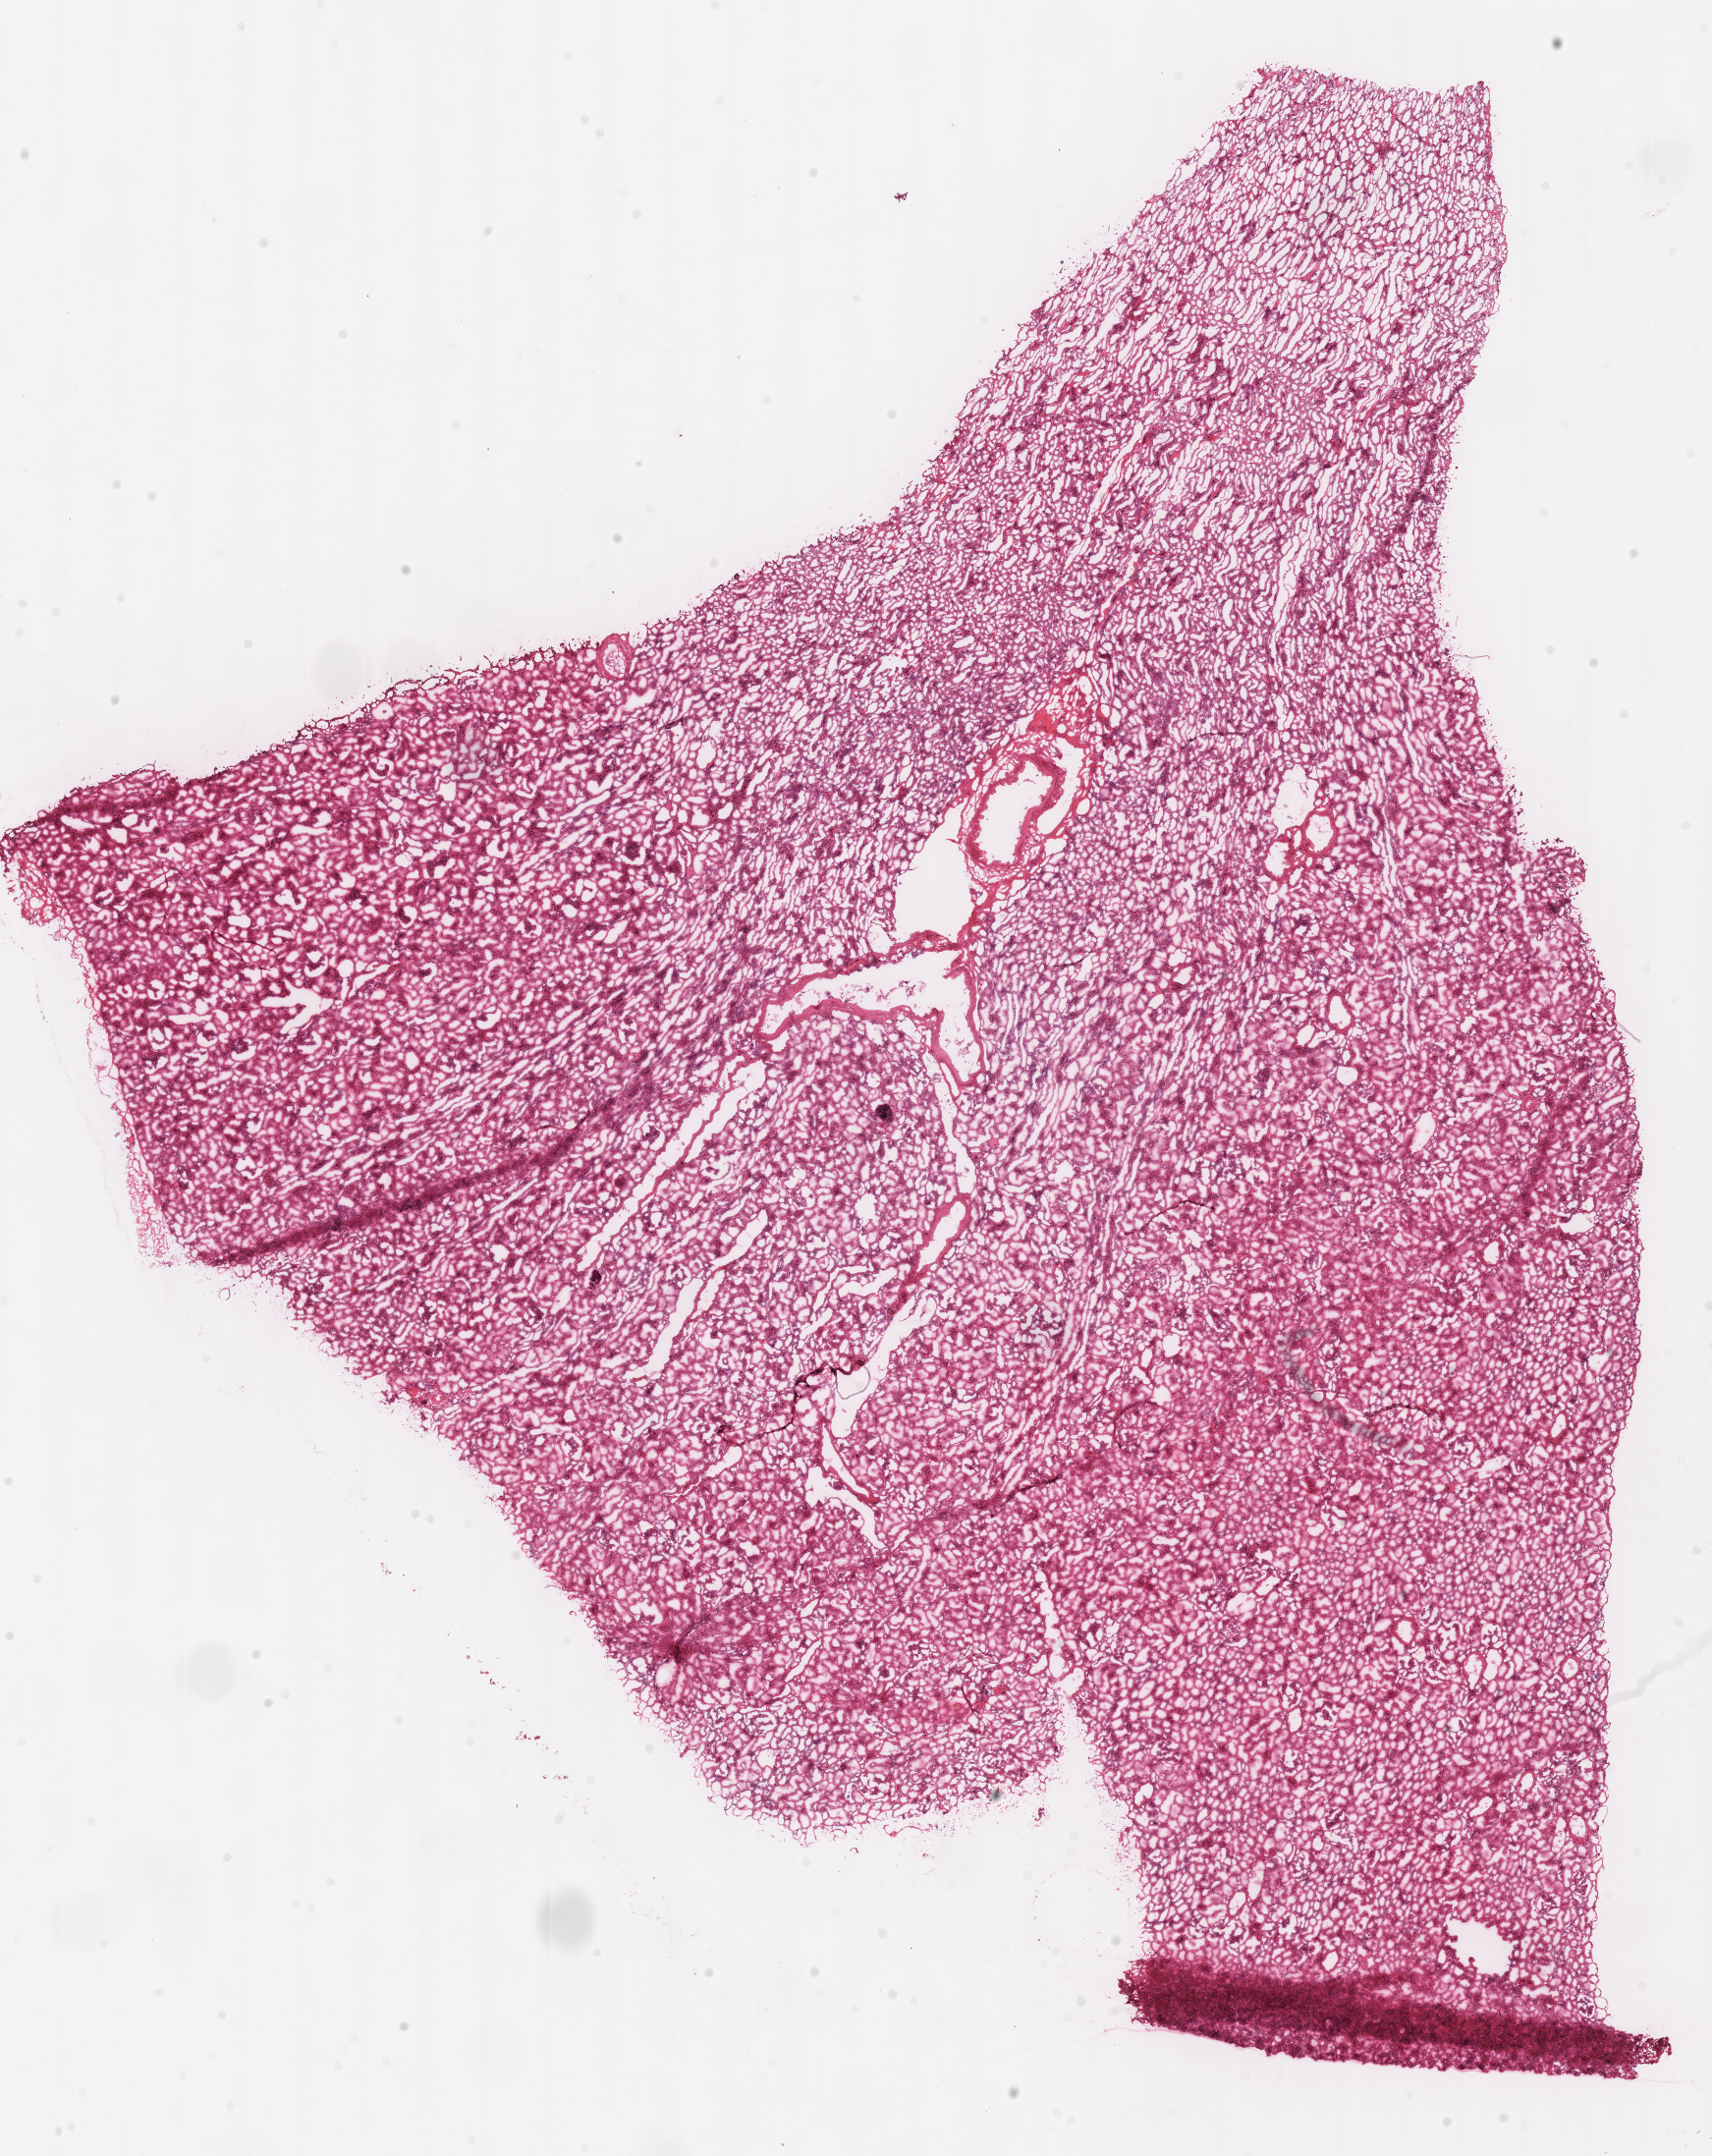
Whole-slide histology image, H&E, whole scanned area (about 13.7 x 17.3 mm) shown as a low-resolution overview; frozen section from the top of the tissue portion; sample: solid tissue normal (non-tumour tissue), kidney. Female patient; age at initial diagnosis 46 years. Inflammatory infiltration, as recorded: lymphocyte infiltration 1%, monocyte infiltration 0%, neutrophil infiltration 0%.
This section: solid tissue normal (non-tumour) sample from the same patient. Patient diagnosis: Renal cell carcinoma, chromophobe type.